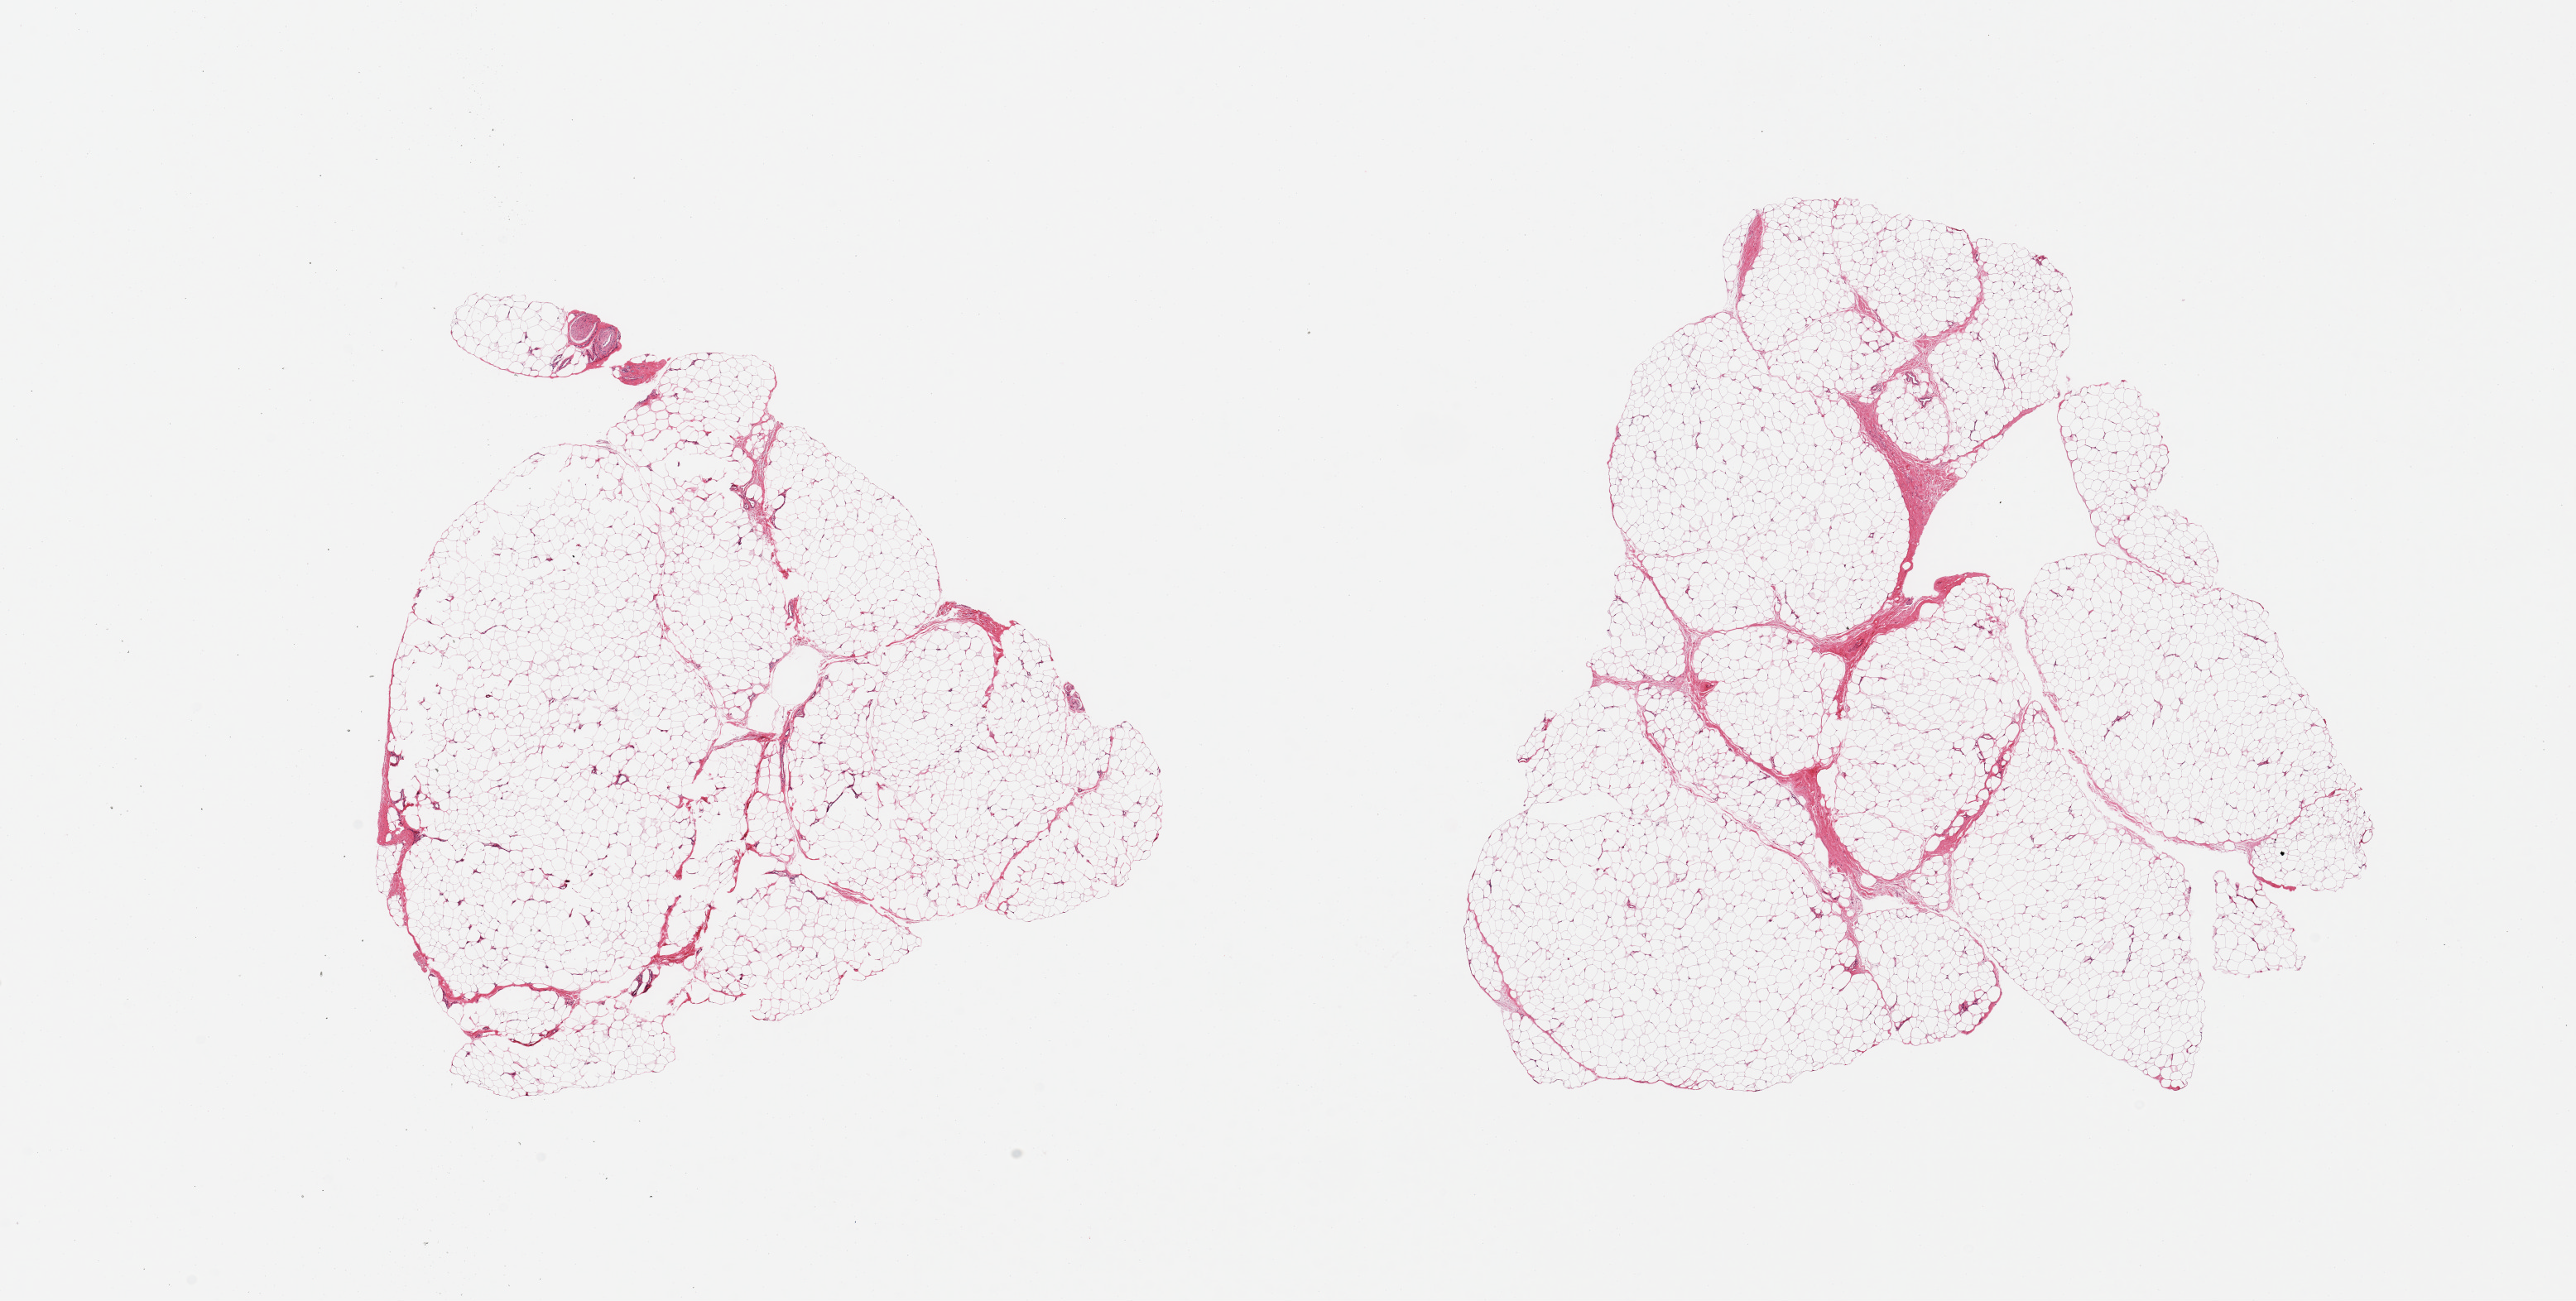
Digitized haematoxylin and eosin-stained section — low-resolution overview of the scanned area, about 24.6 x 12.4 mm. PAXgene-fixed paraffin-embedded (PFPE) section. Sampled site (target tissue): adipose tissue. Tissue donor sample. Donor: female.
Pathologist's review note for this sample: 2 pieces; <5% fibrous content.